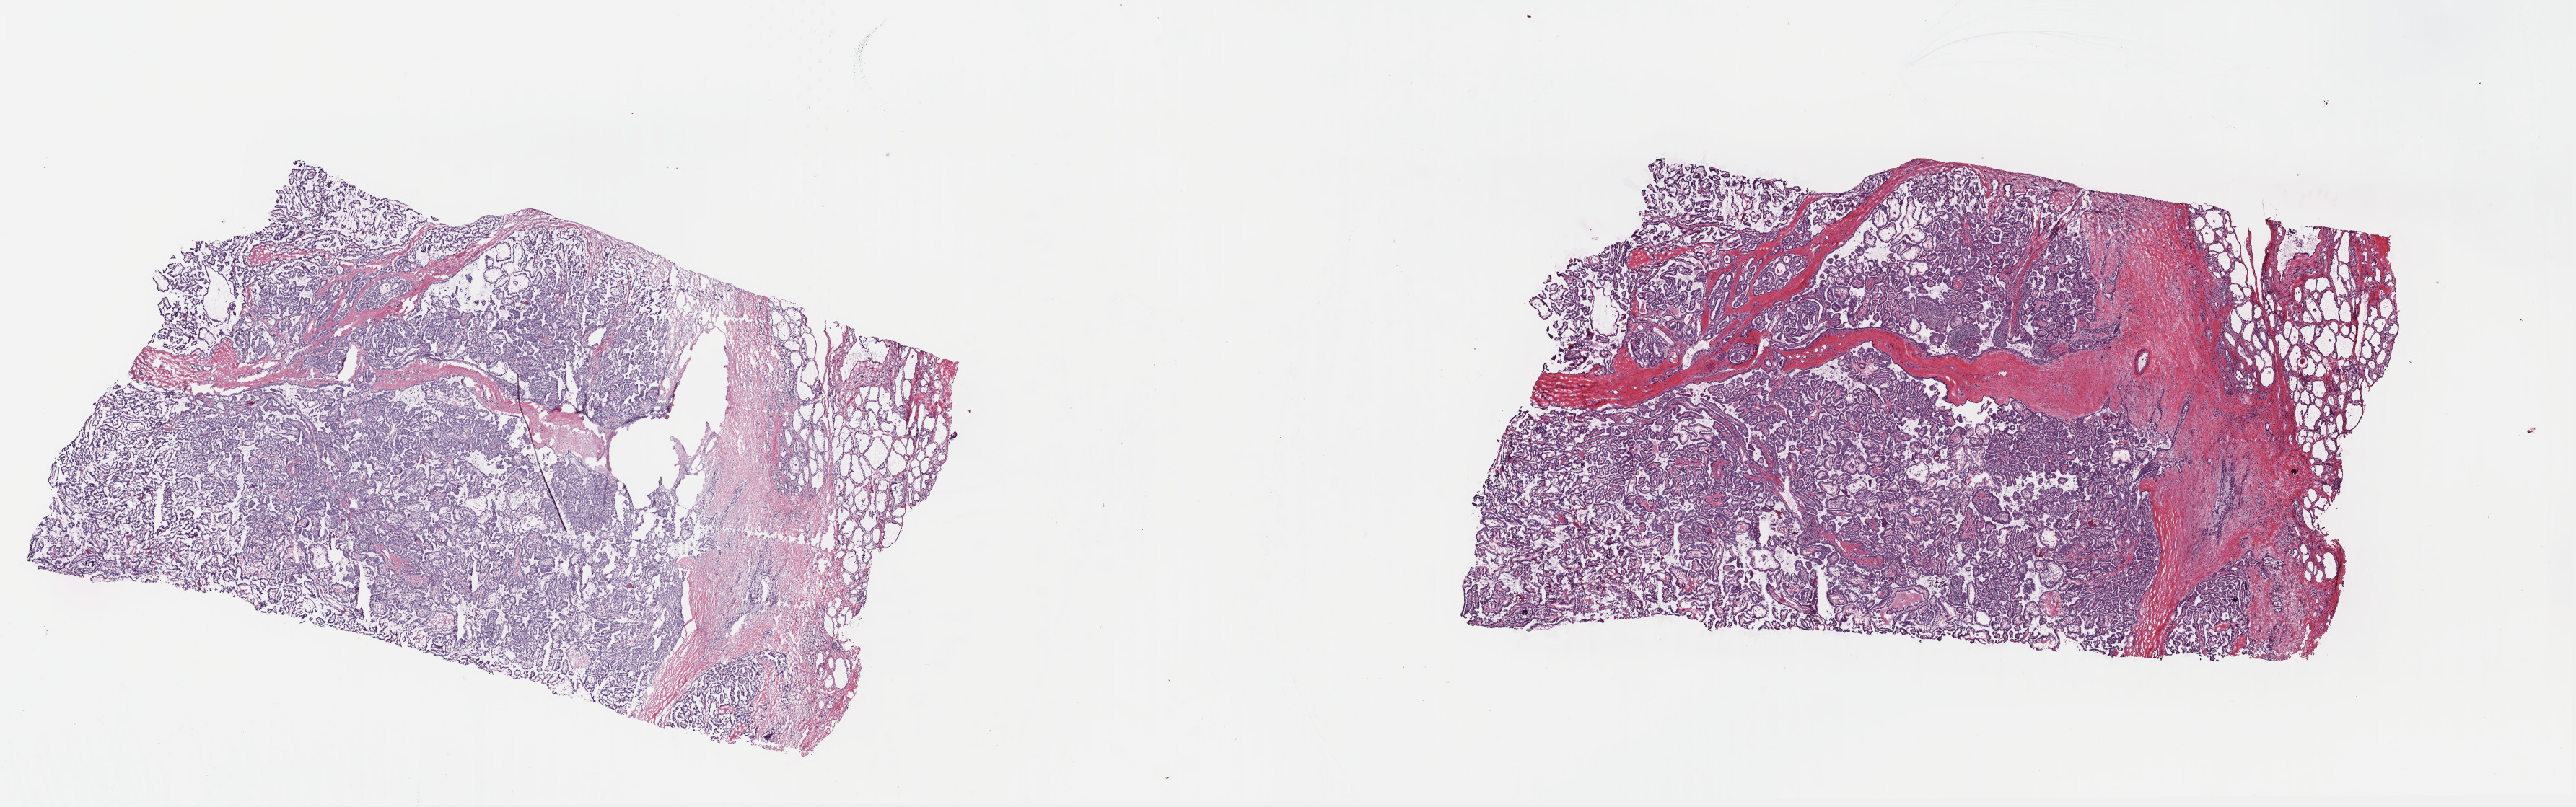
Whole-slide histology image, H&E, shown as a low-resolution overview of the whole scanned area (about 28.1 x 8.8 mm, from a 40x scan); frozen section from the top of the tissue portion; primary tumour sample from the thyroid. Patient: female, age at initial diagnosis 38 years. Composition of this section per pathologist review: tumour cells 70%, tumour nuclei 70%, normal cells 5%, stromal cells 25%, necrosis 0%. Inflammatory infiltration, as recorded: lymphocyte infiltration 5%, monocyte infiltration 0%, neutrophil infiltration 0%.
Laterality: right. AJCC pathologic stage: I (7th edition). Diagnosis: Papillary adenocarcinoma, NOS (thyroid gland).